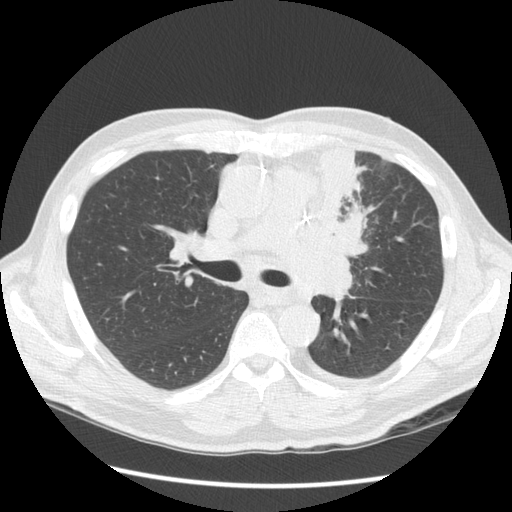
Low-dose screening chest CT, one axial slice. Slice 88 of 136 in the series (ordered by position). Reconstruction kernel STANDARD. 120 kVp. Lung window (W 1500 / L -600 HU). 2.5 mm slice thickness. 512 × 512 image matrix, field of view 360 × 360 mm.
Structures marked on this image (manually delineated by an expert):
- lesion 1 (tumor, upper lobe of left lung): bounding box (x1, y1, x2, y2) in pixels: (304, 145, 369, 304)